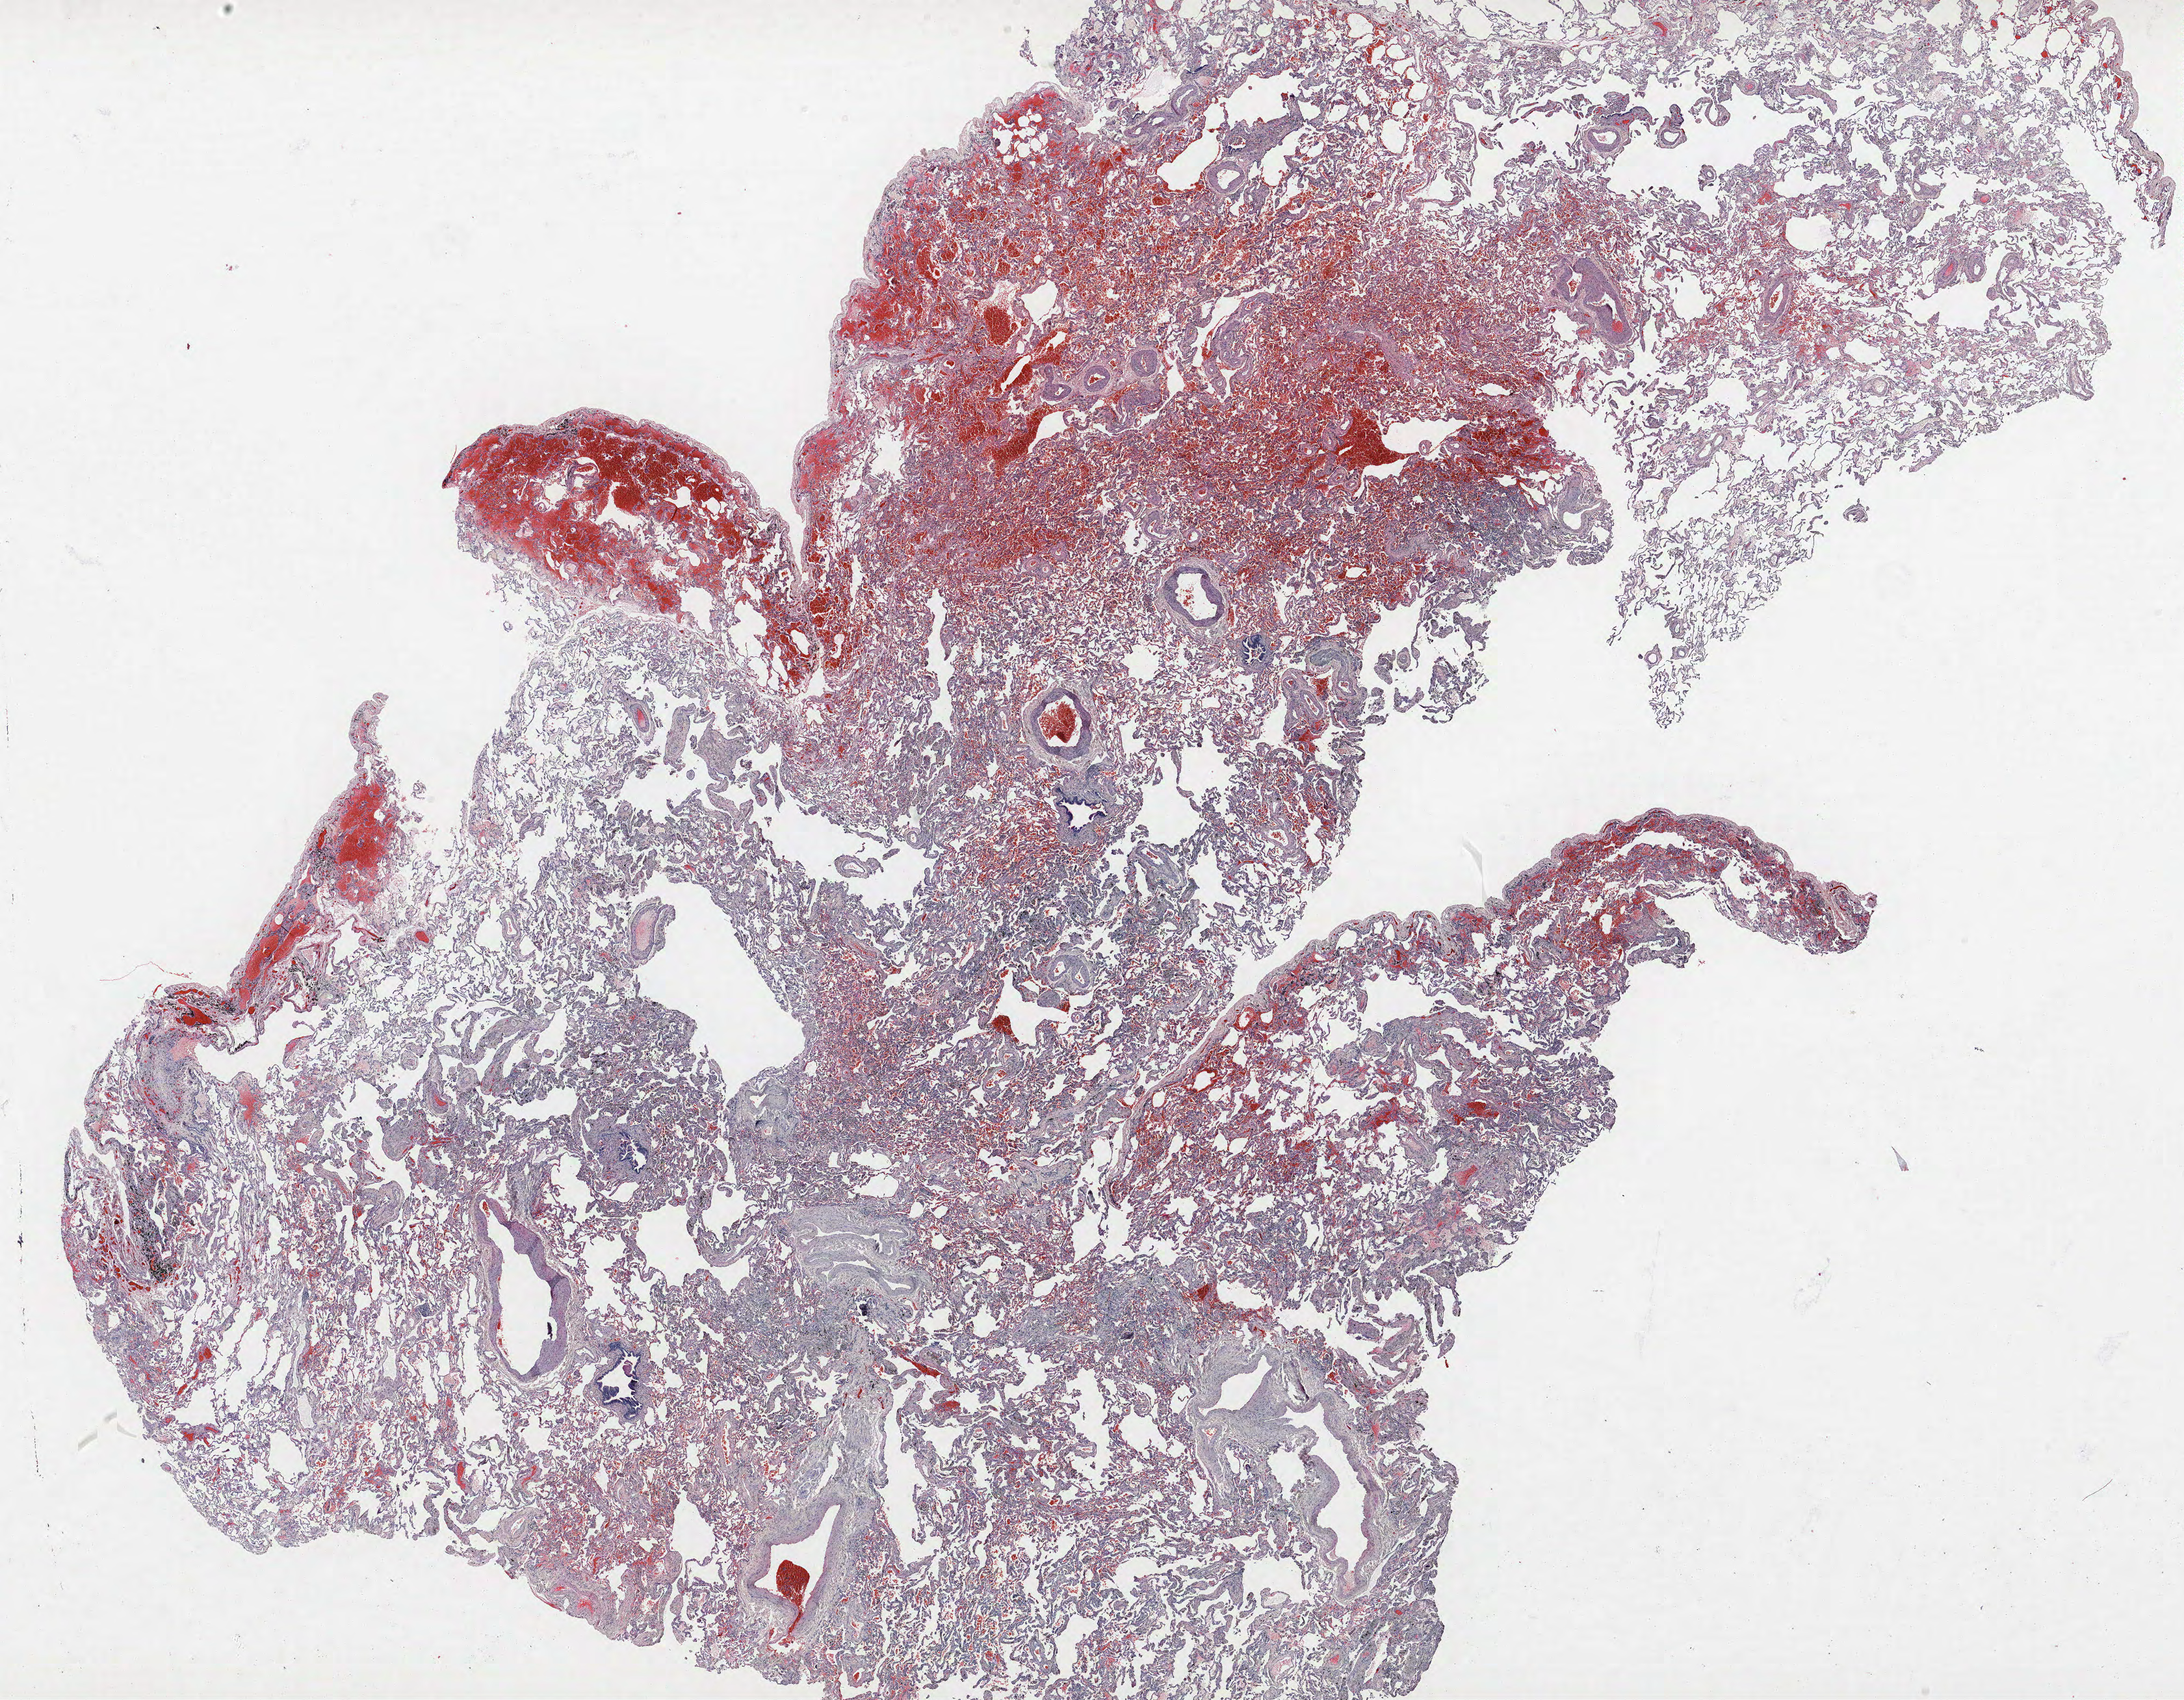
Whole-slide histology image, H&E-stained, shown as a low-resolution overview of the whole scanned area (about 26.9 x 20.9 mm, acquisition: 40x scan); formalin-fixed paraffin-embedded (FFPE) section; lung. Female patient, aged 59 at enrolment. Current smoker at enrolment. Grade: moderately differentiated (G2).
* participant's lung-cancer diagnosis: Squamous cell carcinoma, NOS
* primary tumour location (clinical record): right upper lobe
* stage (AJCC 6th edition): IA
* tumour size (pathology): 28 mm